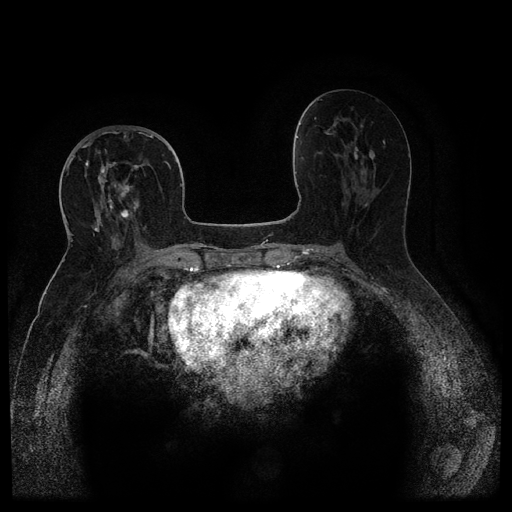
Breast MRI (dynamic contrast-enhanced, multi-phase), one axial slice. Dynamic contrast-enhanced series, time point 2 of 5 at this slice position (early post-contrast). 1.5 T. TE 2.6 ms, TR 5.4 ms. 512 × 512 image matrix, field of view 340 × 340 mm. Female patient, age 68 years.
Structures marked on this image (semi-automatic segmentation, software-assisted and operator-edited):
- breast lesion (labelled 'tumour' in the annotation; benign lesions carry a separate 'benign' label): bounding box [x1, y1, x2, y2] px = [114, 179, 133, 203]
- breast lesion (labelled 'tumour' in the annotation; benign lesions carry a separate 'benign' label): [97, 160, 117, 213]